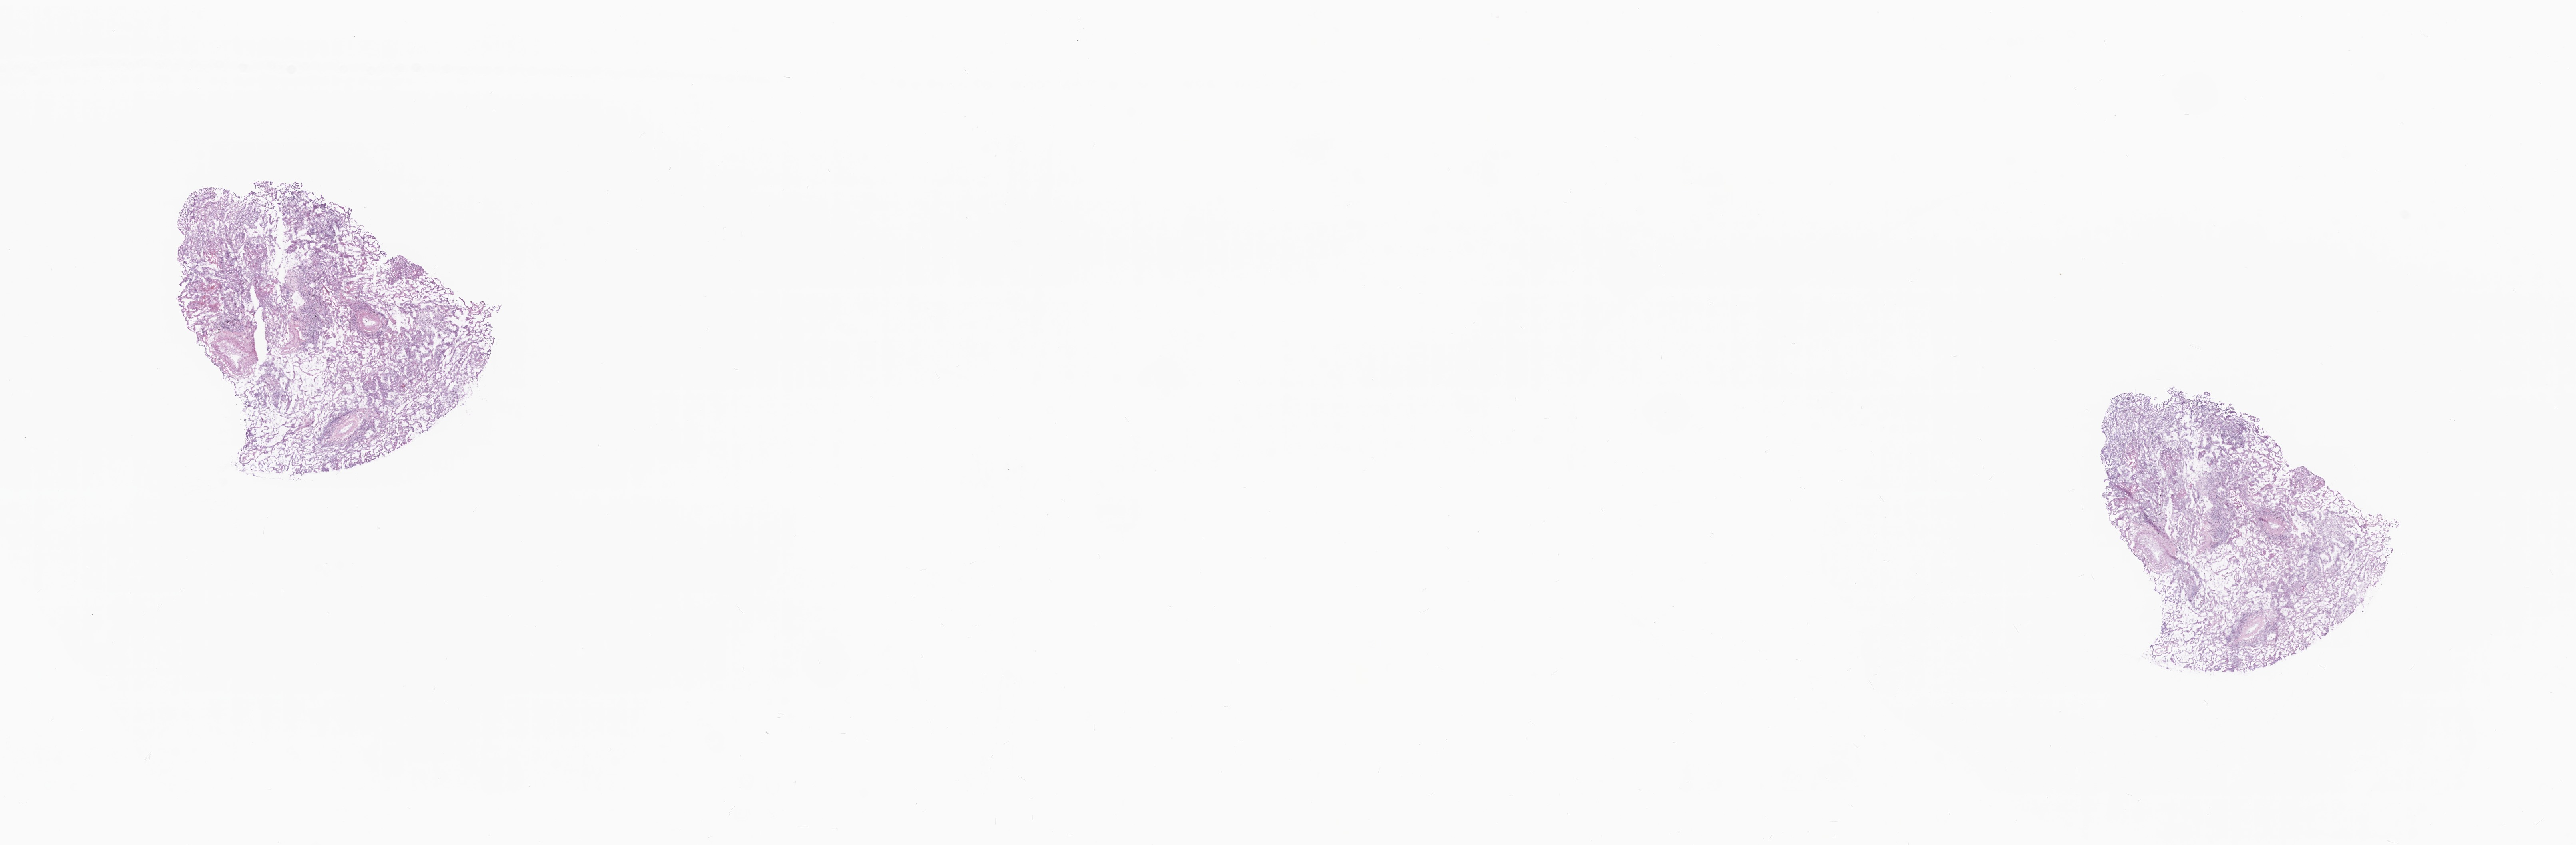
Digitized haematoxylin and eosin-stained section — whole scanned area (about 27.2 x 8.9 mm) shown as a low-resolution overview, frozen section (tissue freezing medium), primary tumor, site: lower lobe of right lung. Male, age 88 years at initial diagnosis. Pathologist review of this section (percent, as recorded): tumor cells 20%, tumor nuclei 60%, stromal cells 5%, necrosis 0%, normal cells 75%. Infiltration values recorded for this section: lymphocyte infiltration 50%, monocyte infiltration 0%, neutrophil infiltration 0%.
Diagnosis: Squamous cell carcinoma, NOS. Section: bottom of the tissue portion.